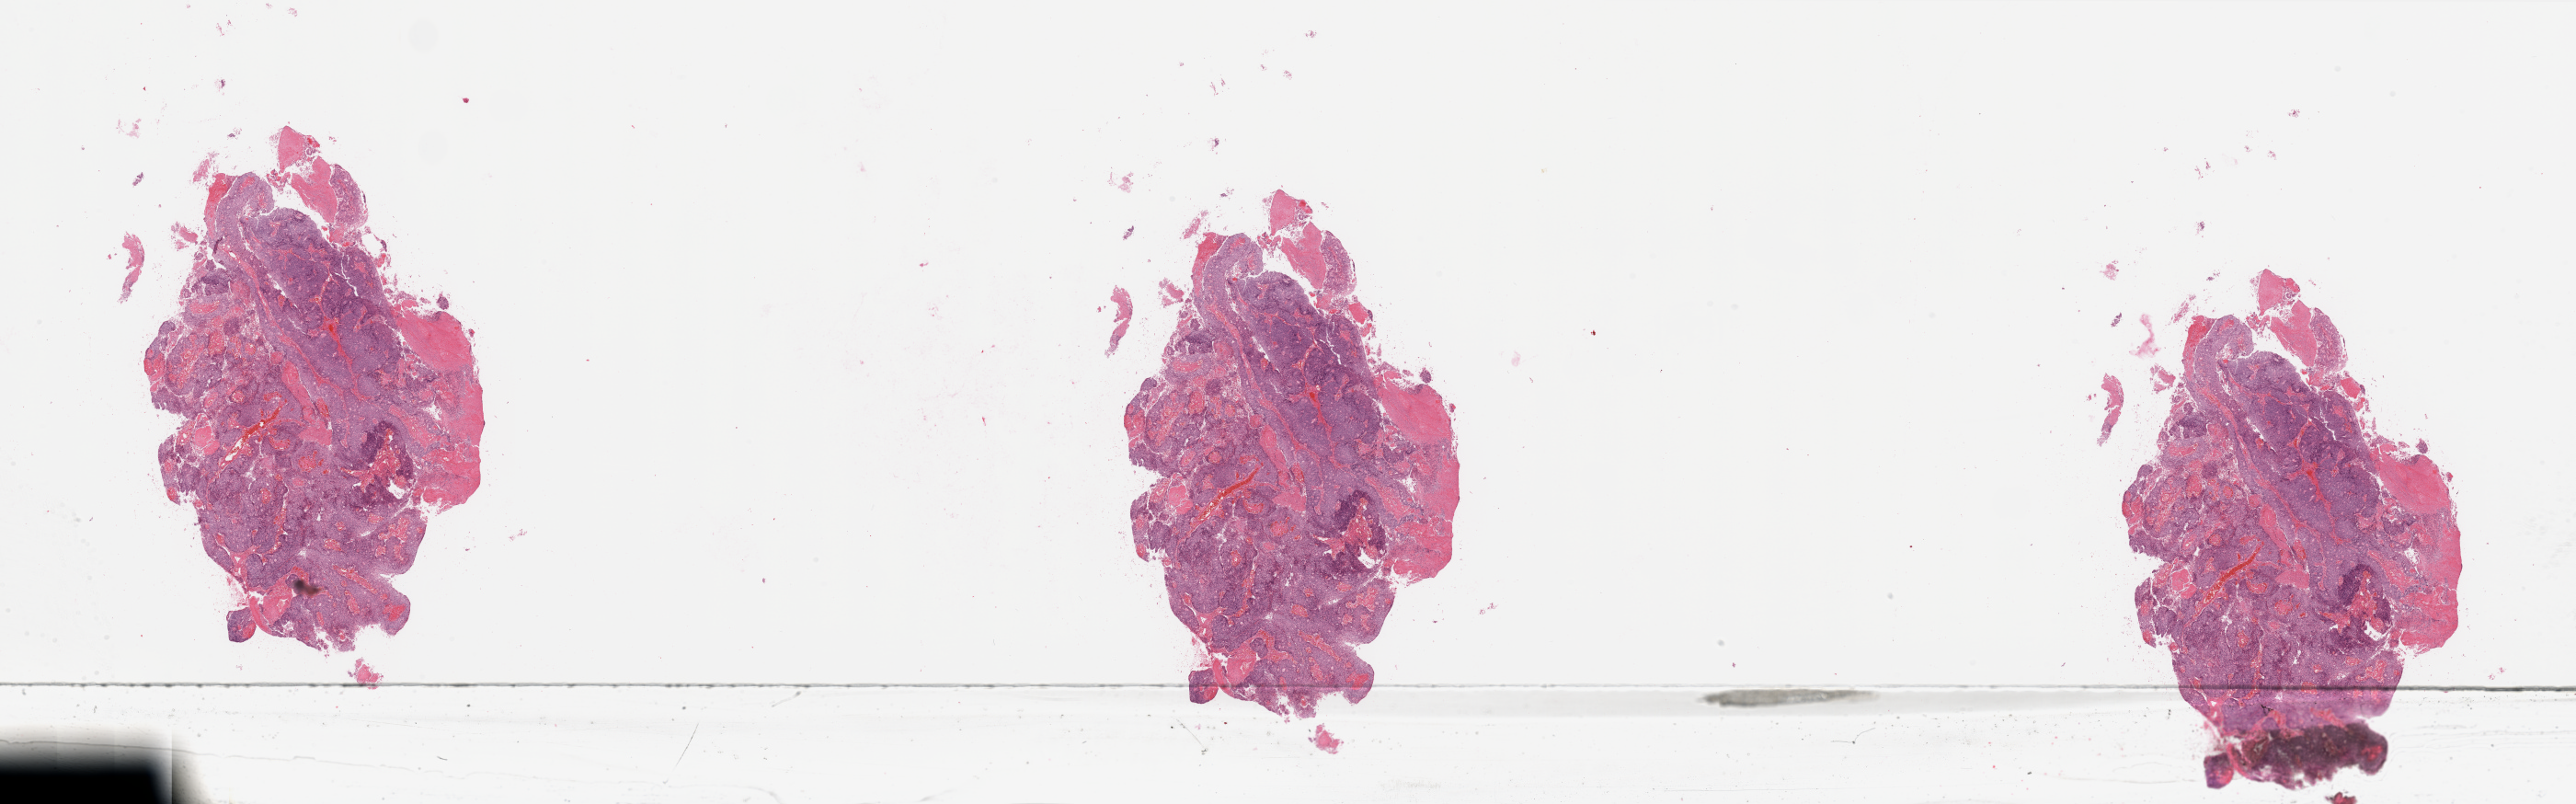
Whole-slide histology image, H&E, low-resolution overview of the scanned area, about 44.3 x 13.8 mm (slide scanned at 20x). Tumour tissue sample, uterus. Female, 53 y/o. Histologic grade: G2 (moderately differentiated).
AJCC pathologic stage: II. Histologic diagnosis: Endometrioid adenocarcinoma, NOS.